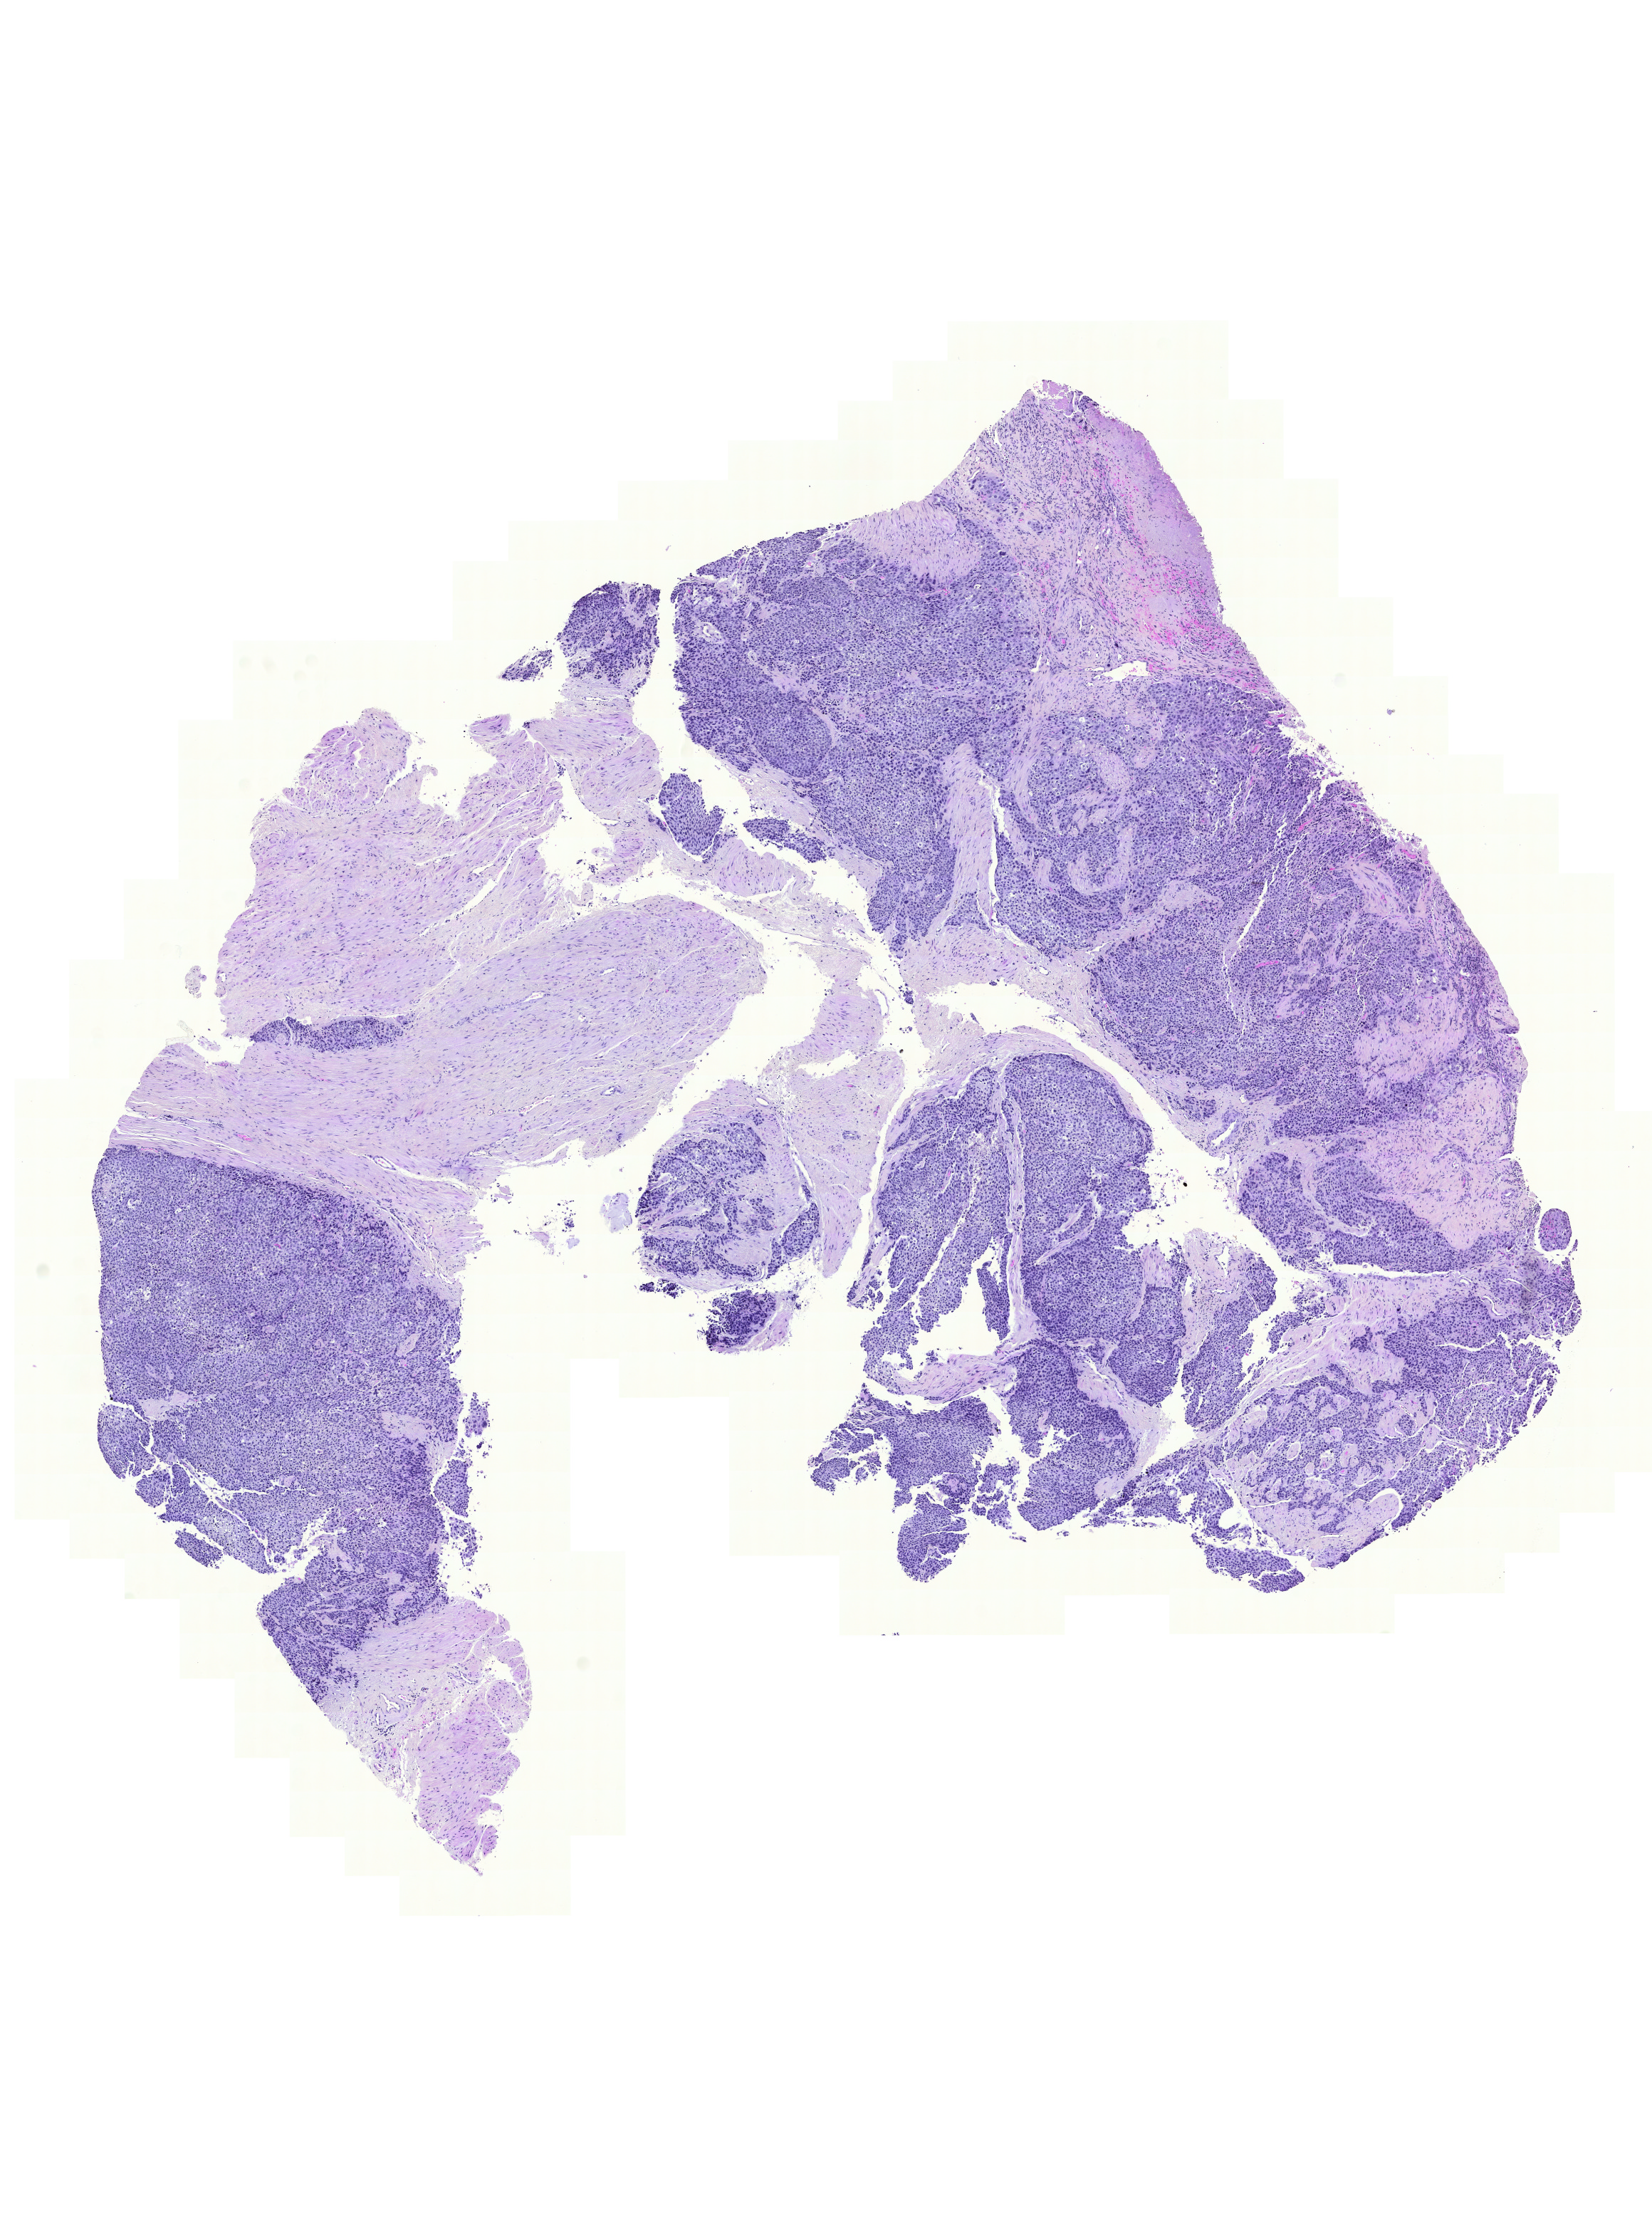
Whole-slide histology image, H&E, whole scanned area (about 8.6 x 11.6 mm, acquisition: 20x scan) shown as a low-resolution overview. Formalin-fixed paraffin-embedded (FFPE) diagnostic section. Sample: primary tumour, bladder. Male, age 77 years at initial diagnosis. Histologic grade: high grade.
- AJCC pathologic stage: IV (6th edition)
- histologic diagnosis: Transitional cell carcinoma